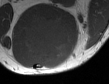
MRI of an extremity soft-tissue mass, one axial slice; slice 35 of 50 in the series (ordered by position); MR volume resampled by the dataset authors to the PET/CT grid (not the native acquisition matrix); 3.27 mm slice thickness; 109 × 84 image matrix, field of view 106 × 82 mm. Male patient. From the clinical record (not read from this slice): histological type: synovial sarcoma; site of the primary tumour: left poplietal fossa.
Outlined on this slice (expert contour drawn on MRI and transferred to this co-registered scan by the dataset authors):
- gross tumour volume (mass): bounding box [x1, y1, x2, y2] px = [23, 16, 72, 65]